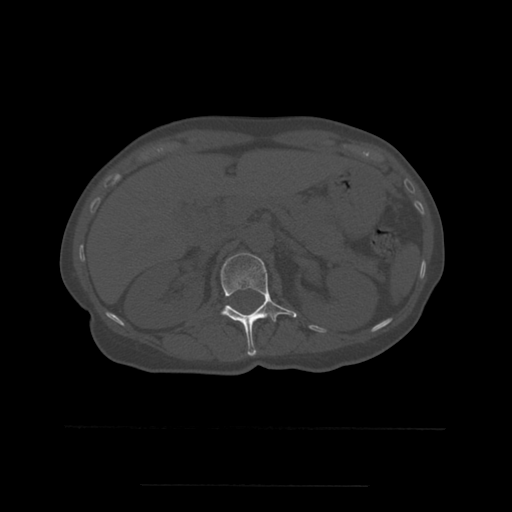
CT including the spine, one axial slice; slice 235 of 544 in the series (ordered by position); bone window (W 1800 / L 400 HU); 1.25 mm slice thickness; 512 × 512 image matrix, field of view 350 × 350 mm. Patient age 58 years. From the clinical record (not read from this slice): primary cancer: lung.
Annotated regions visible in this slice (semi-automatically segmented with operator editing):
- L1 vertebra: bounding box (x1, y1, x2, y2) in pixels: (221, 253, 297, 356)